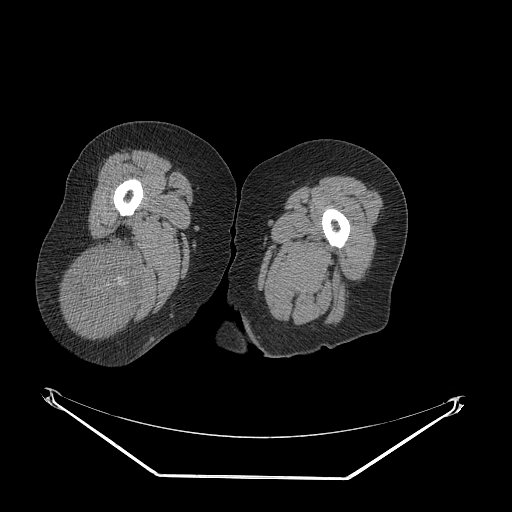
CT of an extremity soft-tissue mass (from a PET/CT study), one axial slice. Slice 35 of 257 in the series (ordered by position). Reconstruction kernel STANDARD. Soft-tissue window (W 400 / L 40 HU). 3.75 mm slice thickness. 512 × 512 image matrix, field of view 500 × 500 mm. Female patient. Case-level facts recorded for this patient, not image findings: histological type: synovial sarcoma; grade: intermediate; site of the primary tumour: right buttock.
Annotated regions visible in this slice (expert contour drawn on MRI and transferred to this co-registered scan by the dataset authors):
- gross tumour volume including surrounding oedema: bounding box [x1, y1, x2, y2] px = [64, 240, 140, 334]
- gross tumour volume (mass): [64, 247, 140, 334]